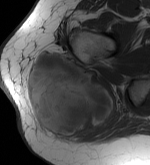
MRI of an extremity soft-tissue mass, one axial slice. Slice 29 of 56 in the series (ordered by position). MR volume resampled by the dataset authors to the PET/CT grid (not the native acquisition matrix). 150 × 165 image matrix, field of view 146 × 161 mm. Female patient. Case-level facts recorded for this patient, not image findings: histological type: epithelioid sarcoma with vascular differentiation; site of the primary tumour: right buttock.
Structures marked on this image (expert contour drawn on MRI and transferred to this co-registered scan by the dataset authors):
- gross tumour volume (mass): box from (x=25, y=51) to (x=115, y=141) px